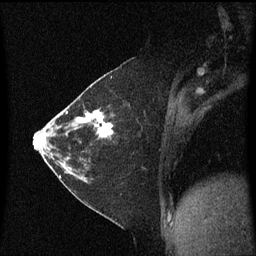
Breast MRI (dynamic contrast-enhanced), one sagittal slice; slice 29 of 60 in the series (ordered by position); dynamic contrast-enhanced series, image 2 of 3 at this slice position (ordered by acquisition); 1.5 T; TE 4.2 ms, TR 8.4 ms; 256 × 256 image matrix. Patient: female, 36 years. From the clinical record (not read from this slice): setting: breast cancer imaged before/during neoadjuvant chemotherapy; receptor status: HR-positive, HER2-negative.
Structures marked on this image (semi-automatic segmentation, software-assisted and operator-edited):
- analysis volume of interest (the breast-tissue region the enhancement analysis was run in; not a lesion): bounding box <66,102,114,179> (left, top, right, bottom; pixels)
- tumour enhancement mask (voxels above the 70 % enhancement threshold inside the analysis volume of interest): <77,110,114,139>